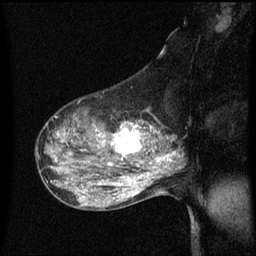
Breast MRI (dynamic contrast-enhanced), one sagittal slice; slice 39 of 60 in the series (ordered by position); dynamic contrast-enhanced series, image 2 of 3 at this slice position (ordered by acquisition); 1.5 T; TE 4.2 ms, TR 8.4 ms; 2 mm slice thickness; 256 × 256 image matrix, field of view 200 × 200 mm. Female patient, age 50 years.
Outlined on this slice (semi-automatically segmented with operator editing):
- analysis volume of interest (the breast-tissue region the enhancement analysis was run in; not a lesion): bounding box [x1, y1, x2, y2] px = [100, 120, 153, 171]
- tumour enhancement mask (voxels above the 70 % enhancement threshold inside the analysis volume of interest): [108, 122, 153, 169]